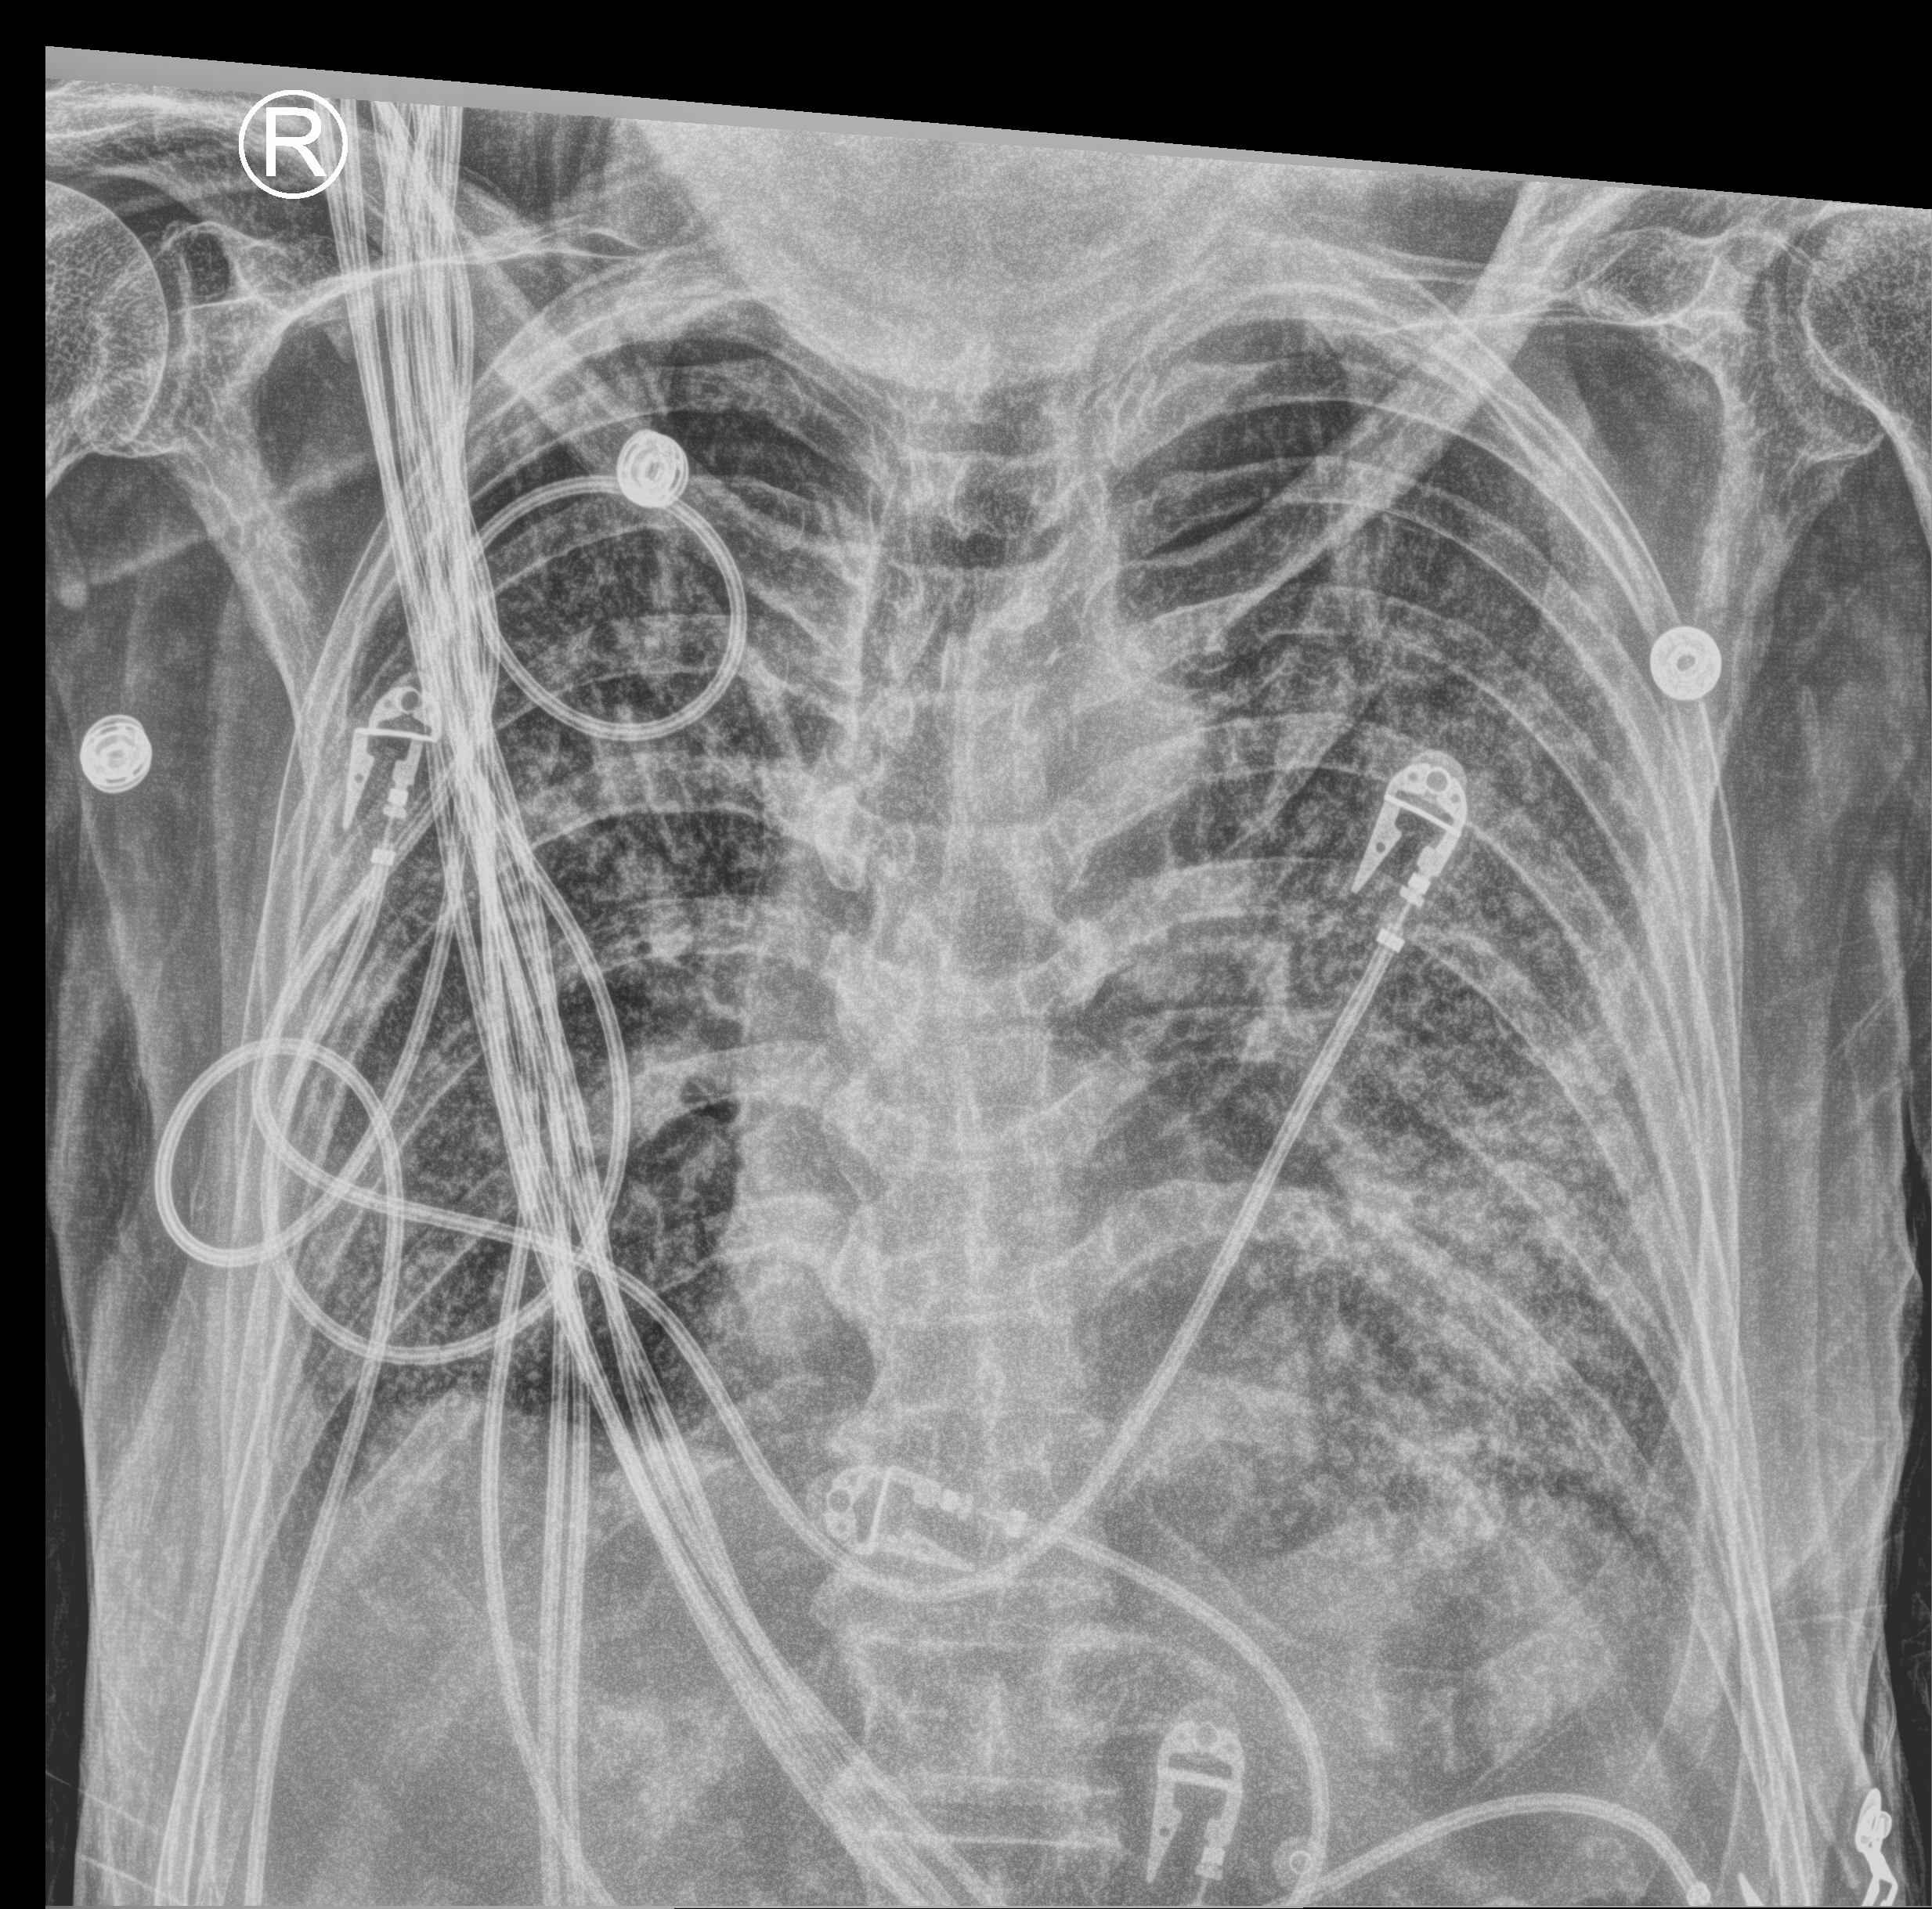
Bedside chest radiograph (computed radiography), anteroposterior (AP) projection. Patient hospitalised with COVID-19; male, aged 60–74 years.
From the hospital-stay record, not from the radiograph (when in the stay this image was taken is not recorded): admitted to intensive care during this hospital stay: yes; other chronic lung disease (admission record): no.